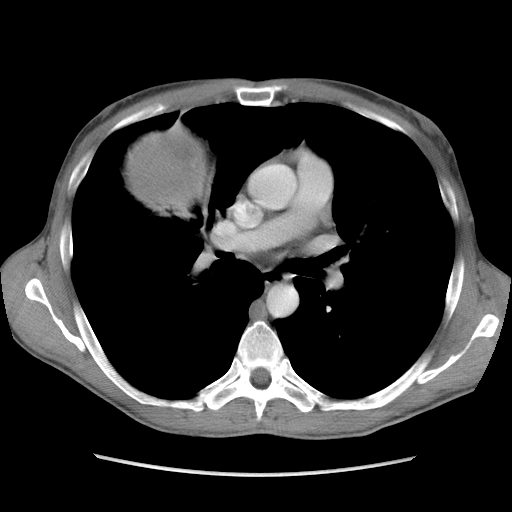
Contrast-enhanced abdominal CT, one axial slice. Position 106 of 115 along the scan axis. Soft-tissue window (W 400 / L 40 HU). 5 mm slice thickness. 512 × 512 image matrix, field of view 360 × 360 mm. Male patient. Case-level facts recorded for this patient, not image findings: diagnosis: adrenocortical carcinoma; tumour side: right adrenal; Ki-67 index: 13 %; stage (as recorded): 3.
Annotated regions visible in this slice (semi-automatically segmented with operator editing):
- mass: box from (x=127, y=133) to (x=202, y=203) px